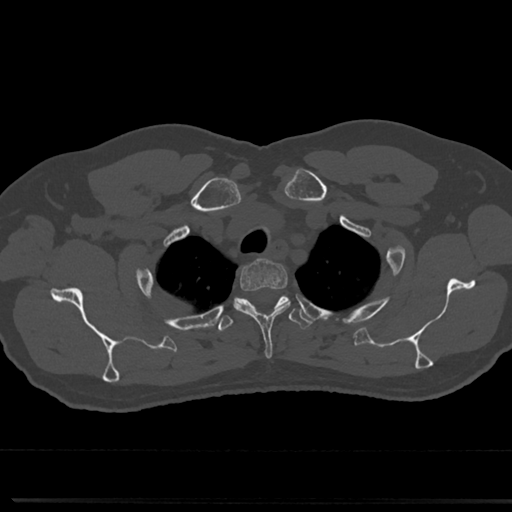
CT including the spine, one axial slice; position 617 of 817 along the scan axis; reconstruction kernel Br40s/3; 120 kVp; bone window (W 1800 / L 400 HU); 0.5 mm slice thickness; 512 × 512 image matrix, field of view 355 × 355 mm. Male patient, age 61 years. From the clinical record (not read from this slice): primary cancer: prostate.
Structures marked on this image (semi-automatically segmented with operator editing):
- T2 vertebra: box from (x=237, y=261) to (x=288, y=317) px
- T3 vertebra: (x=214, y=293)–(x=313, y=334)